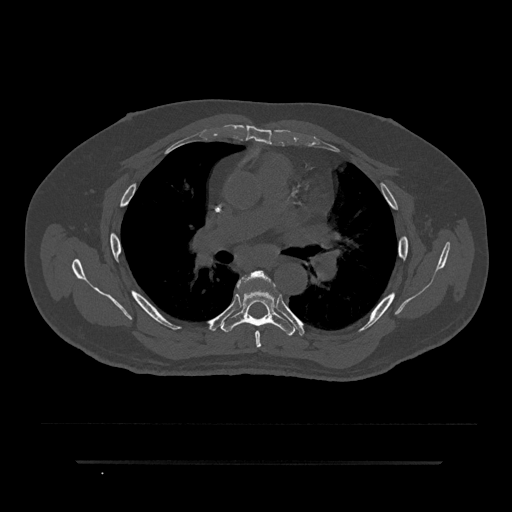
CT including the spine, one axial slice; position 543 of 797 along the scan axis; reconstruction kernel Br40s/3; bone window (W 1800 / L 400 HU); 0.5 mm slice thickness; 512 × 512 image matrix, field of view 464 × 464 mm. Patient: male, 59 years. Case-level facts recorded for this patient, not image findings: primary cancer: bile ducts.
Outlined on this slice (semi-automatic segmentation, software-assisted and operator-edited):
- T5 vertebra: bounding box (x1, y1, x2, y2) in pixels: (236, 271, 275, 348)
- T6 vertebra: (221, 277, 294, 336)